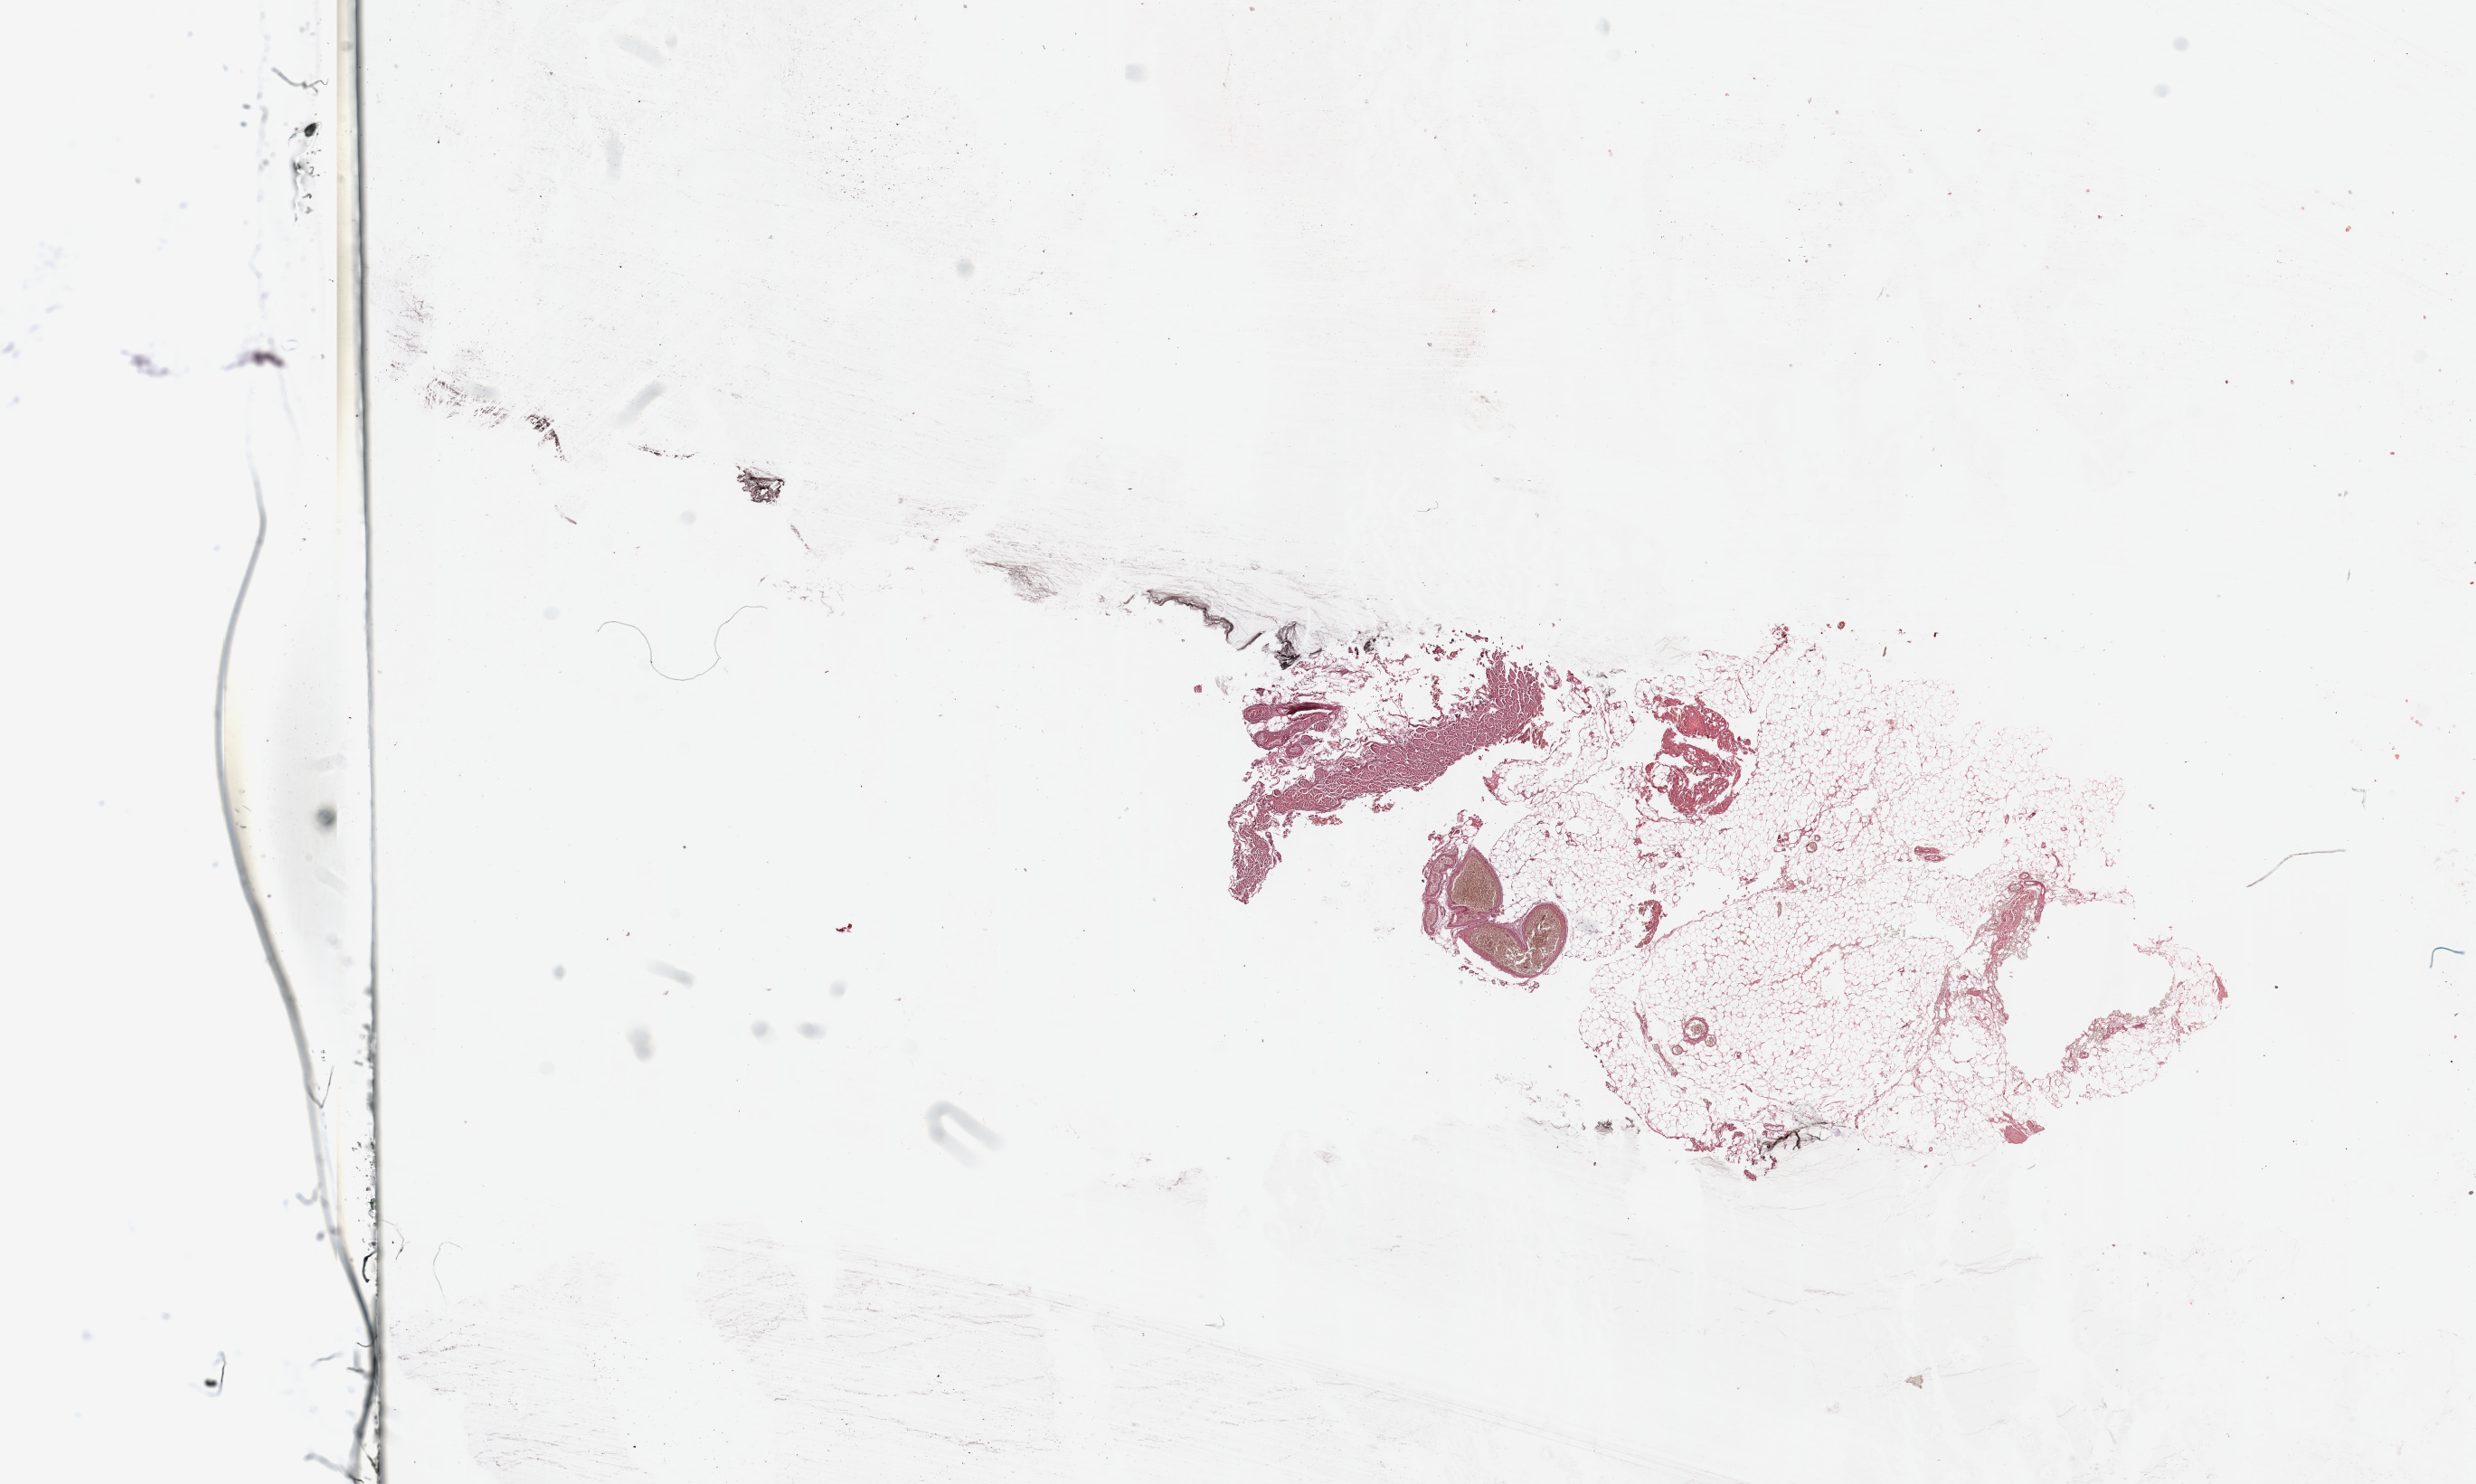
Hematoxylin and eosin (H&E) stained whole-slide image — shown as a low-resolution overview of the whole scanned area (about 21.7 x 13.0 mm). Normal (non-tumour) tissue sample. 77-year-old female patient.
- this section: normal (non-tumour) tissue from the same patient
- patient diagnosis (cohort enrolment): sarcoma (site not recorded at cohort level)